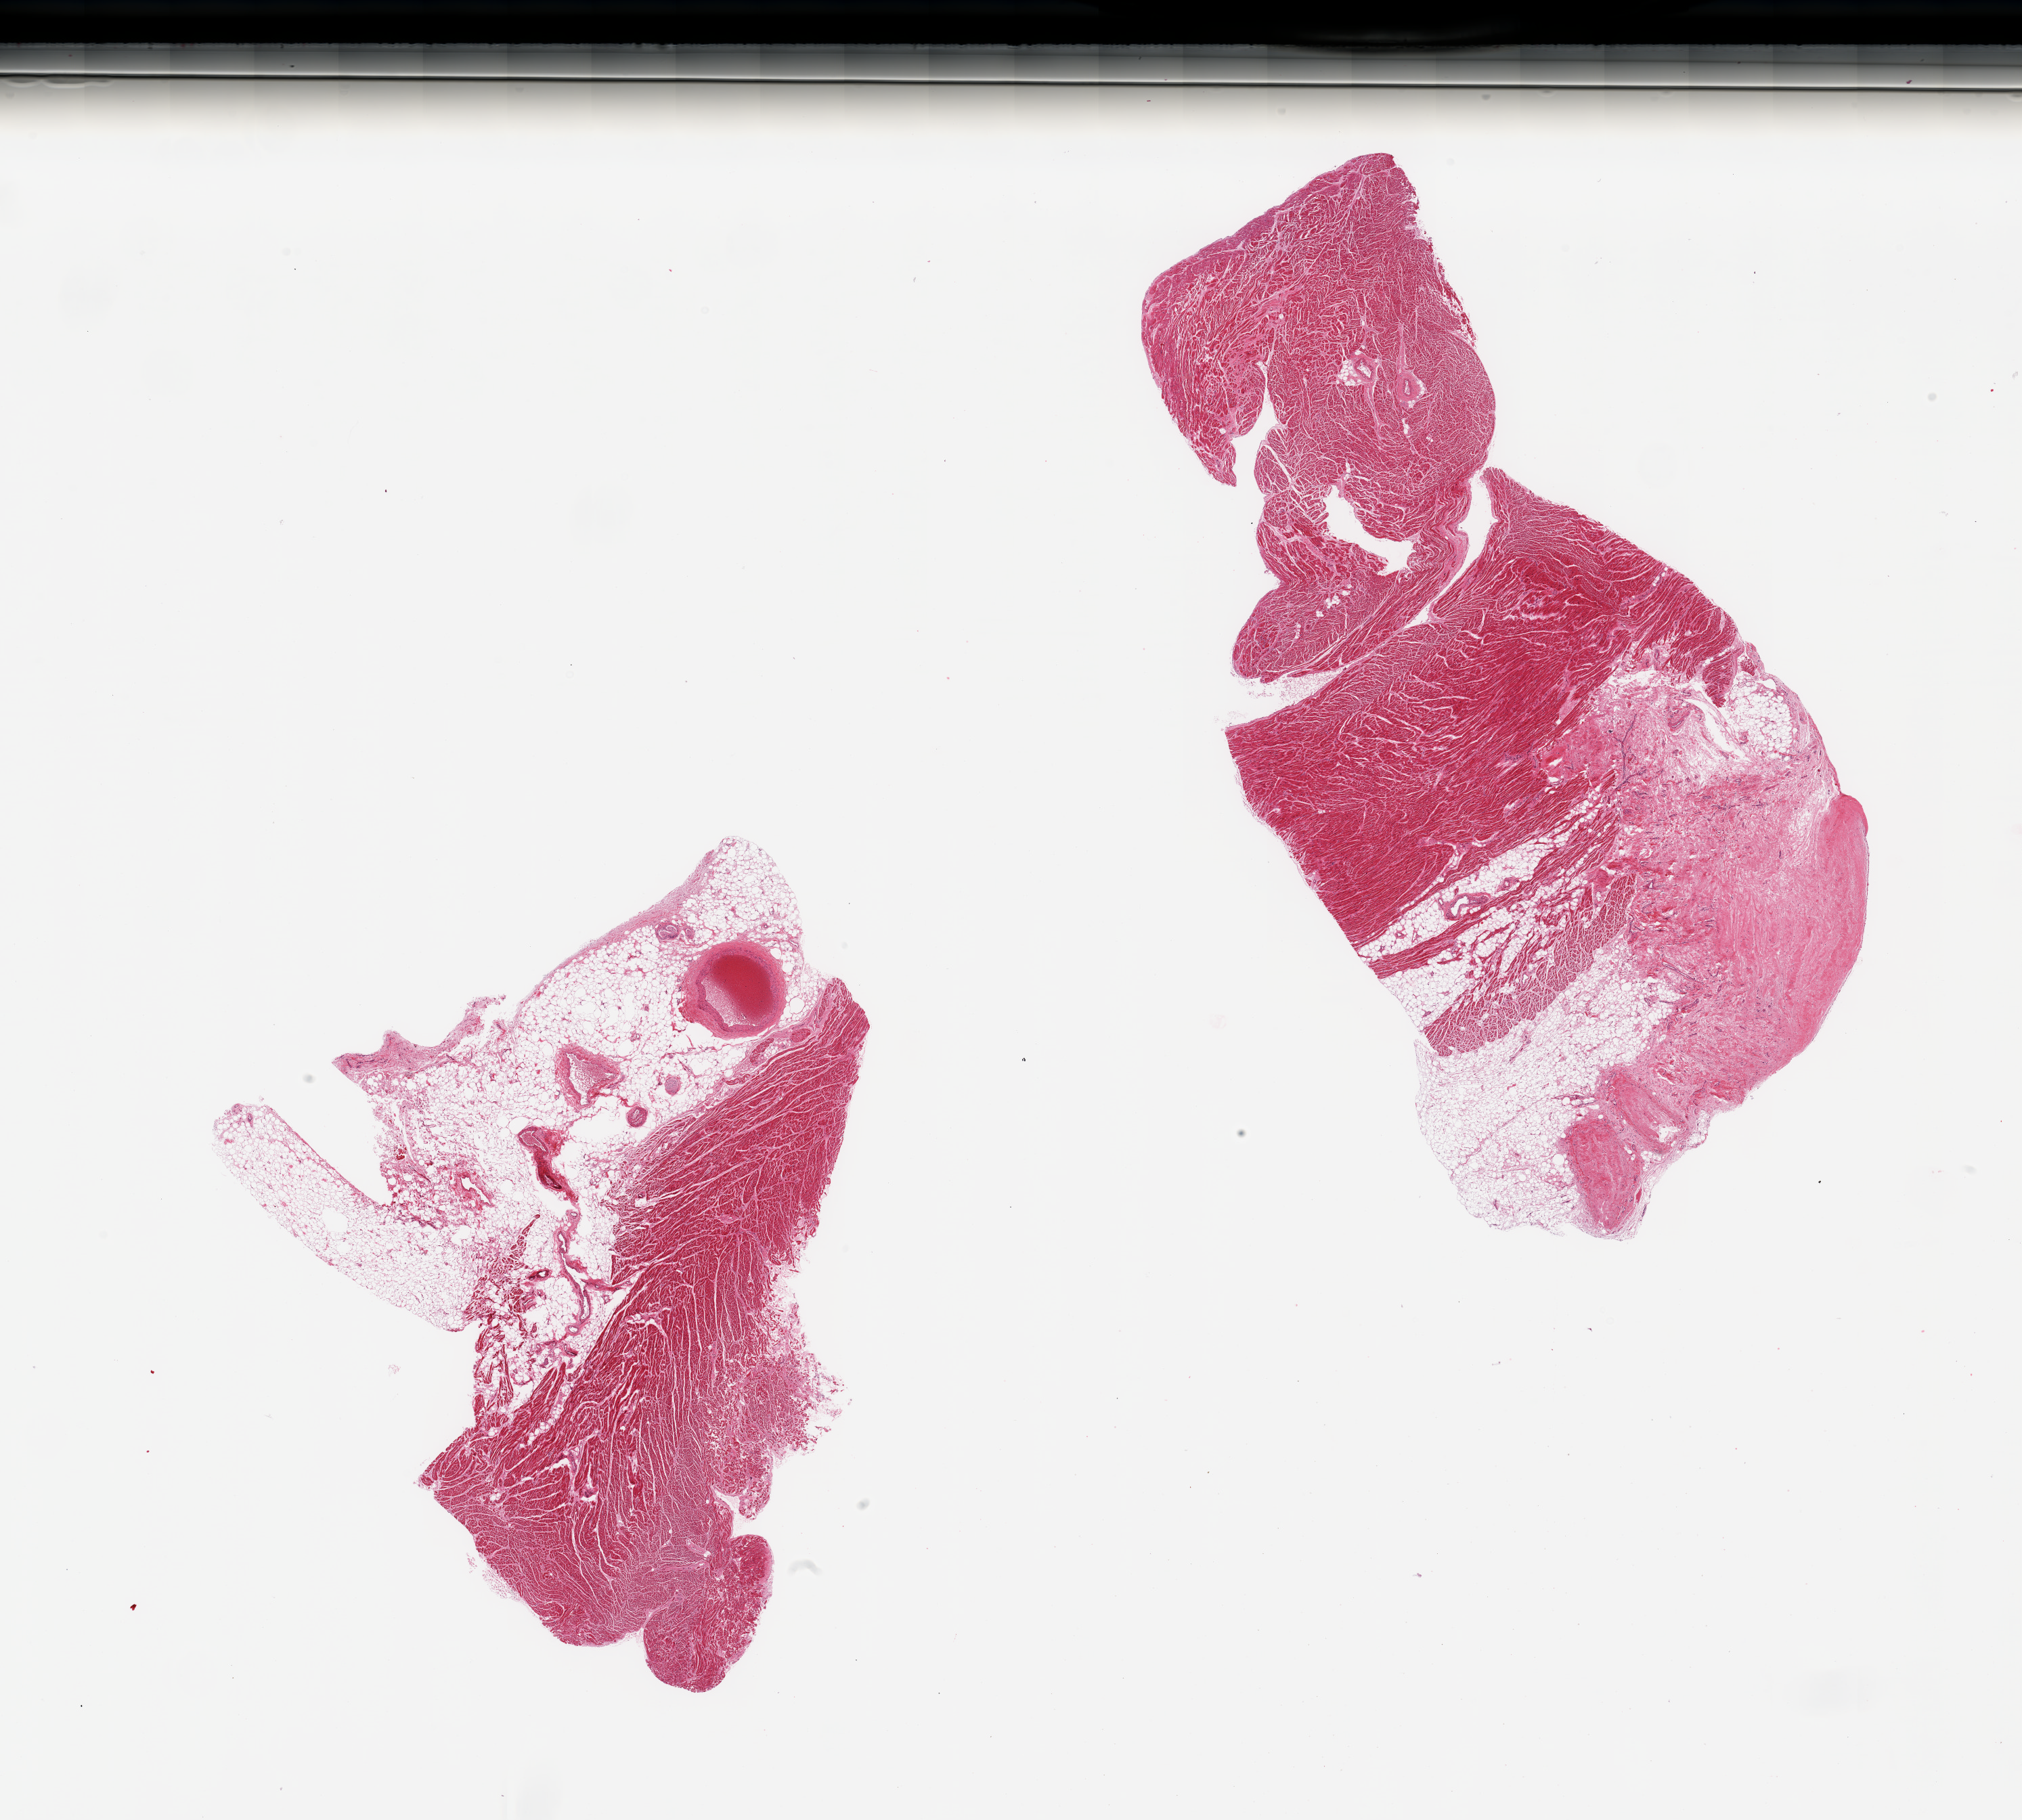
Whole-slide image, hematoxylin and eosin (H&E) stain, shown as a low-resolution overview of the whole scanned area (about 23.6 x 21.3 mm), PAXgene-fixed, paraffin-embedded tissue, sampled site (target tissue): heart, tissue donor sample. Male donor.
Pathologist's review note for this sample: 2 pieces; 1 has 50% epicardial fat; other has 50% fibrous & fatty epicardial tissue.